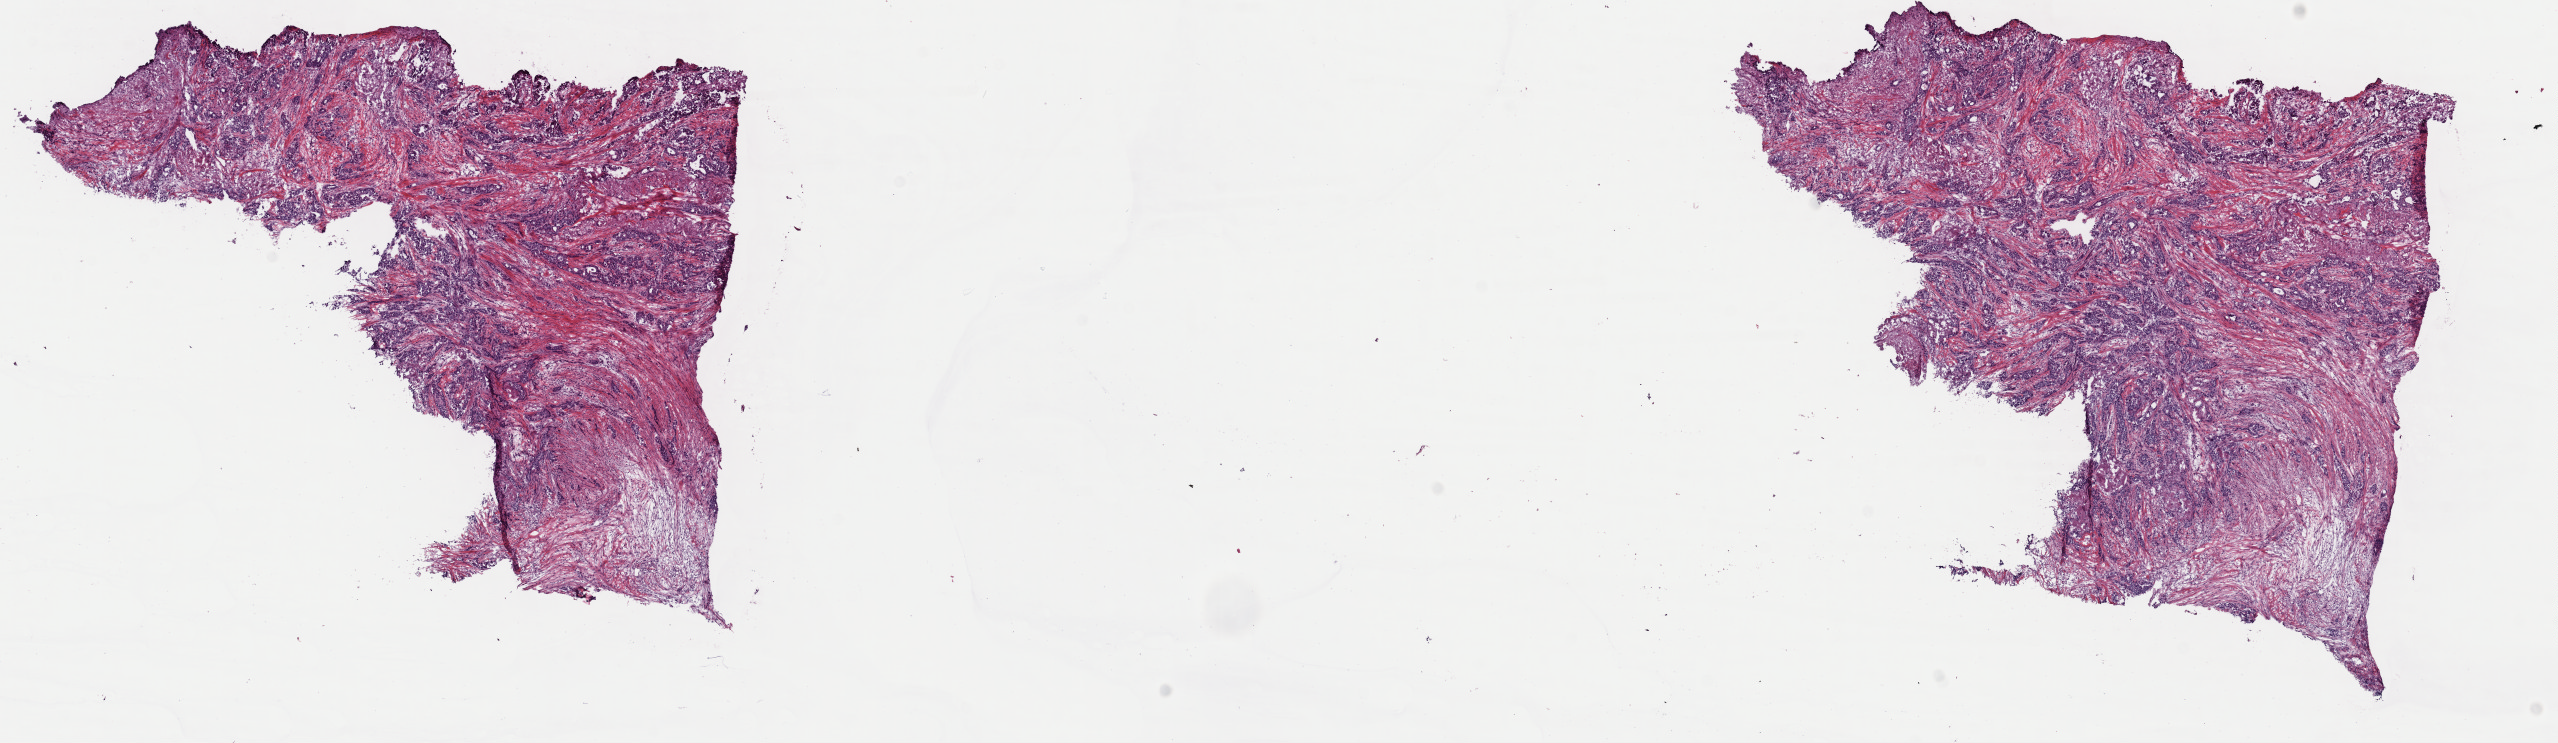
Digitized Hematoxylin and eosin (H&E) stained tissue section (whole slide) — whole scanned area (about 20.2 x 5.9 mm) shown as a low-resolution overview, frozen section, sample: primary tumour, breast. Female patient; age at initial diagnosis 76 years.
Histologic diagnosis: Infiltrating duct carcinoma, NOS.